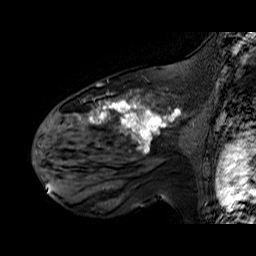
Breast MRI (dynamic contrast-enhanced), one sagittal slice; slice 40 of 60 in the series (ordered by position); dynamic contrast-enhanced series, time point 2 of 6 at this slice position (early post-contrast); 1.5 T; TE 6.3 ms, TR 32.9 ms; 4 mm slice thickness; 256 × 256 image matrix, field of view 200 × 200 mm. Female patient. From the clinical record (not read from this slice): setting: breast cancer imaged before/during neoadjuvant chemotherapy; receptor status: HER2-positive.
Outlined on this slice (semi-automatic segmentation, software-assisted and operator-edited):
- analysis volume of interest (the breast-tissue region the enhancement analysis was run in; not a lesion): bounding box (x1, y1, x2, y2) in pixels: (48, 92, 195, 174)
- tumour enhancement mask (voxels above the 100 % enhancement threshold inside the analysis volume of interest): (71, 96, 176, 152)